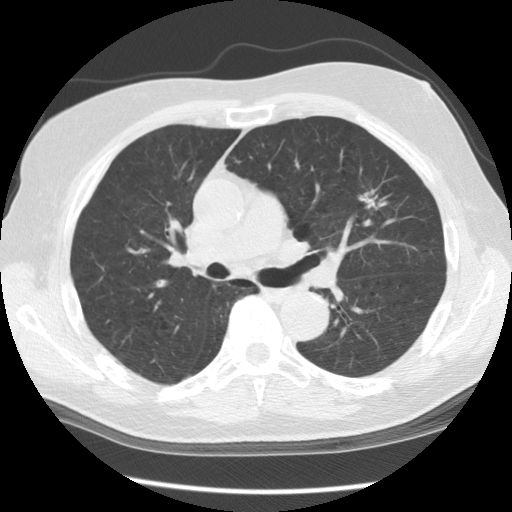
Axial slice from a low-dose chest CT screening exam. Second annual screen. Lung window (W 1500 / L -600 HU). Standard (soft-tissue) reconstruction kernel (STANDARD). 140 kVp. 512 × 512 image matrix. Male, age 70 years at enrolment. Current smoker at enrolment.
Expert reader's lesion annotation, bounding box <341,179,401,234> (left, top, right, bottom; pixels). The screening reader recorded 3 non-calcified nodules or masses ≥4 mm on this exam; which of them this box marks is not recorded.